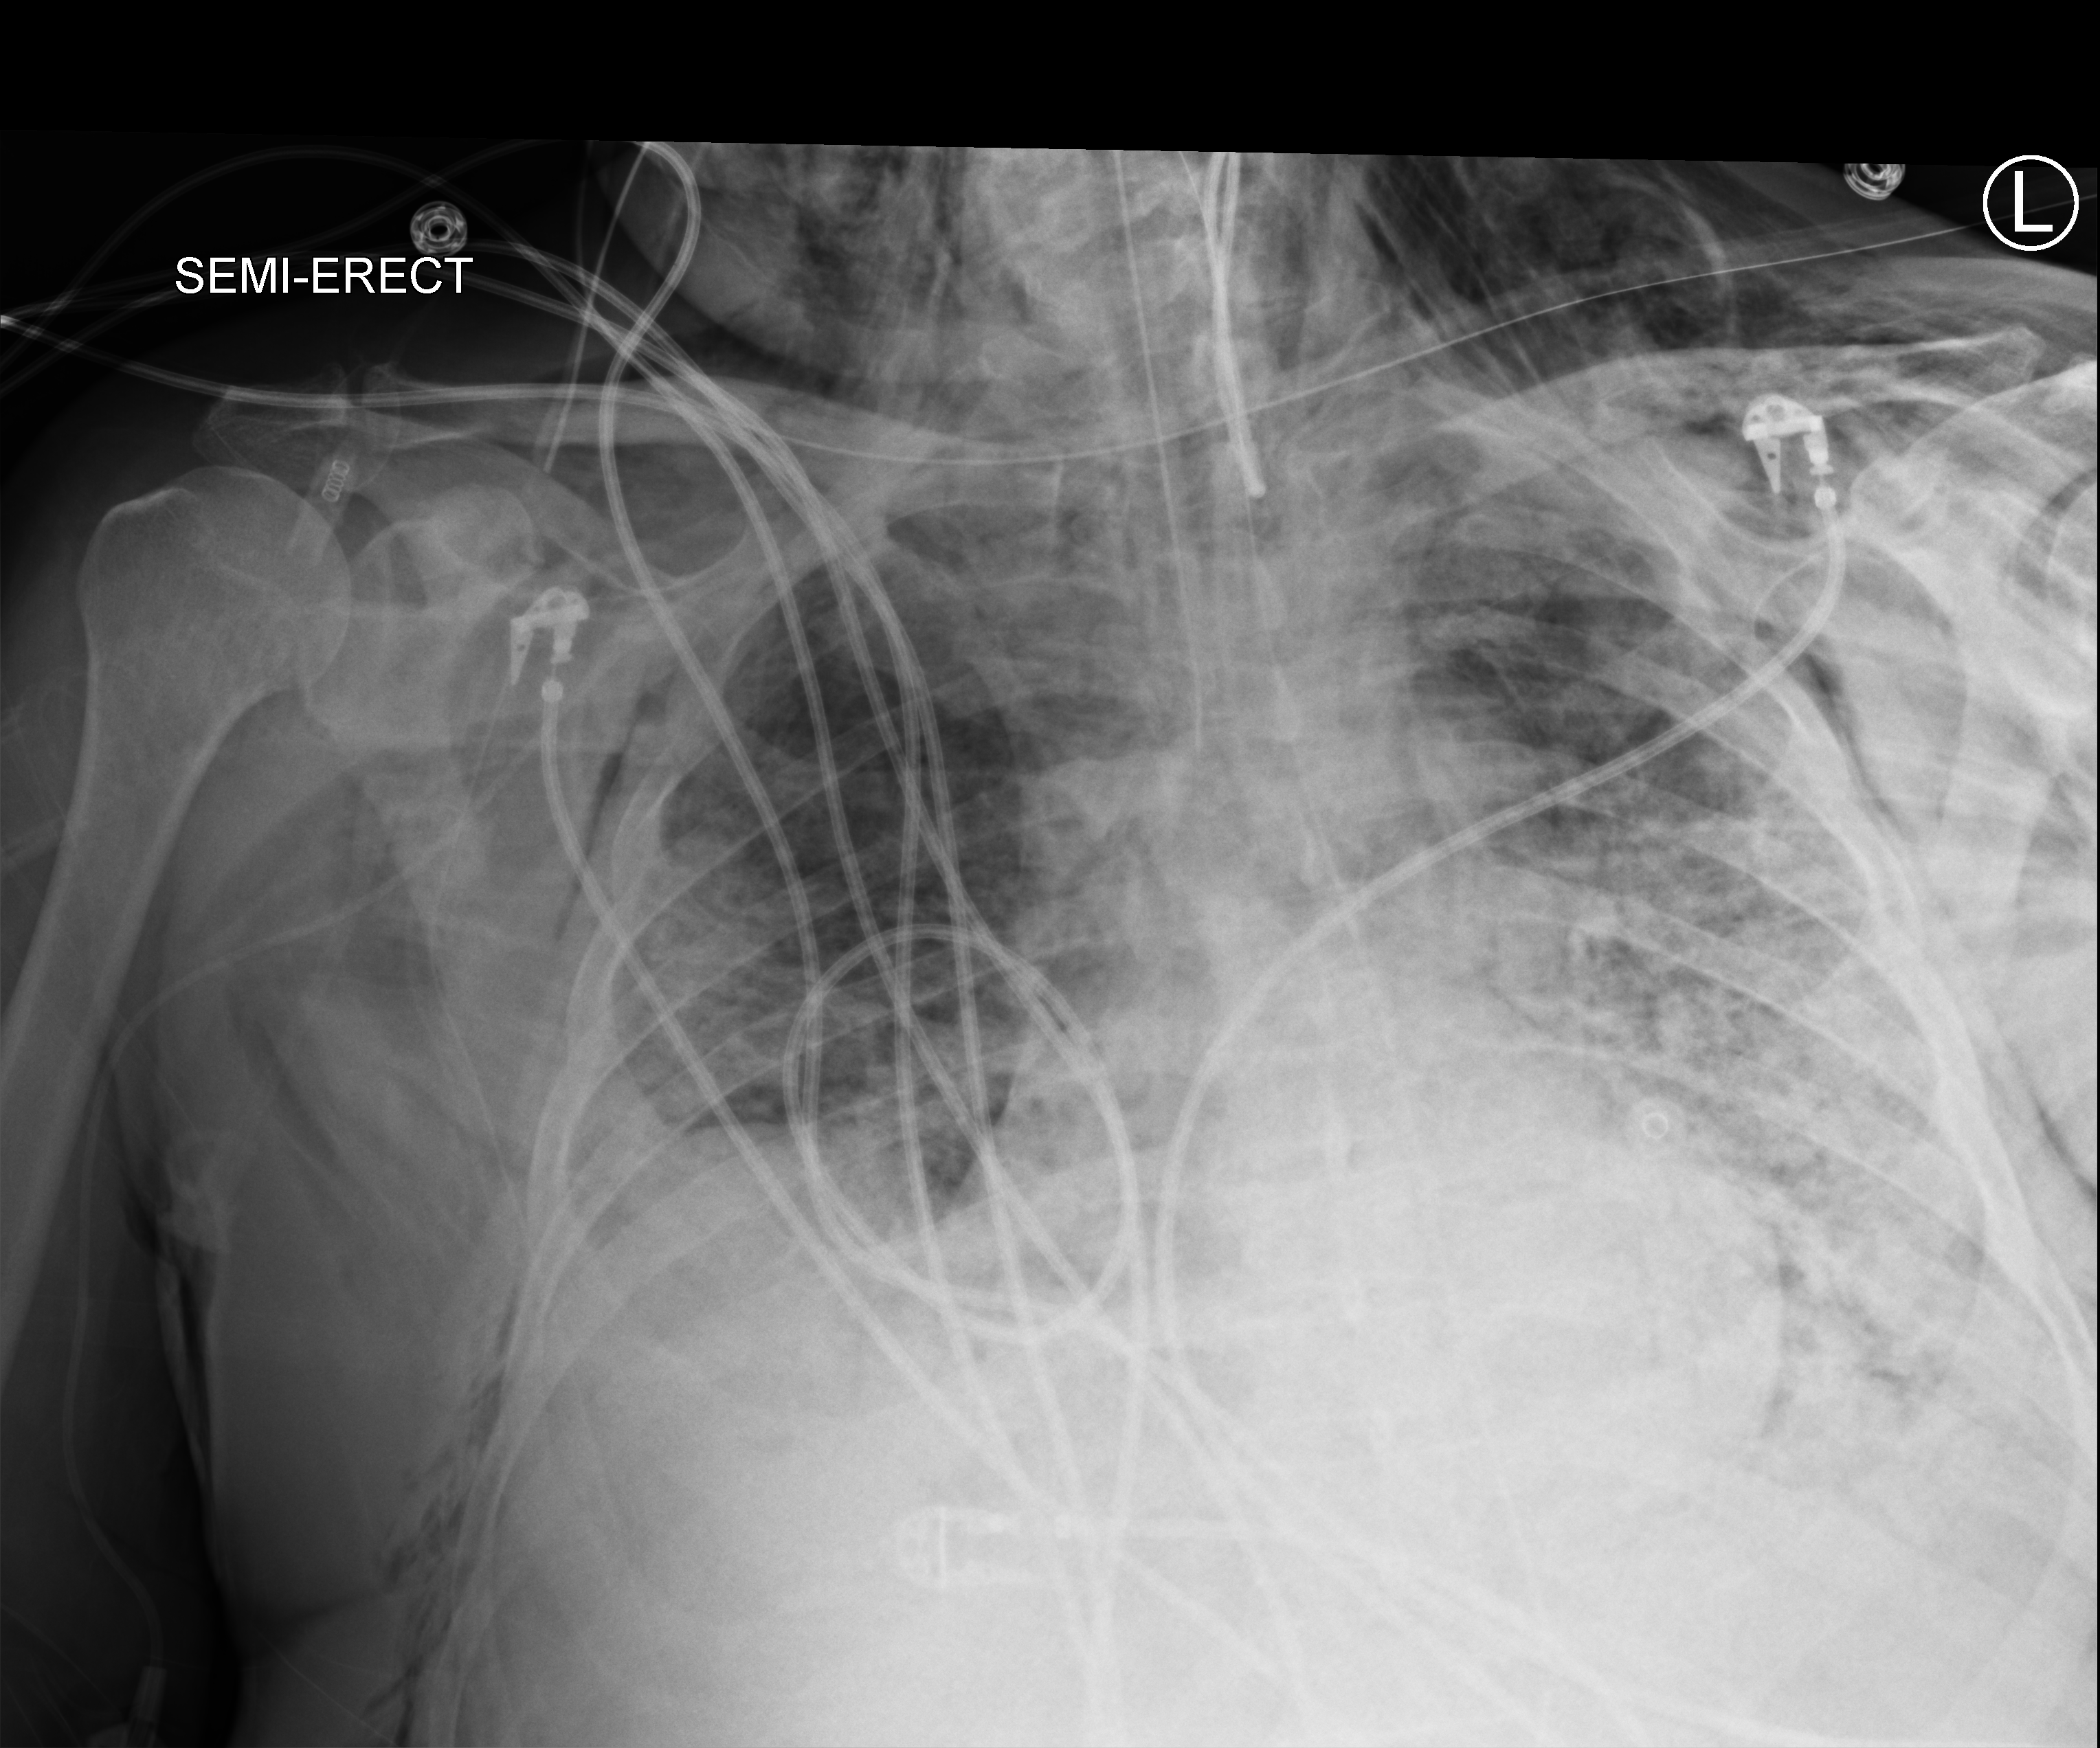
Portable chest radiograph; anteroposterior (AP) projection. Male patient hospitalised with COVID-19, age 60–74 years.
Hospital-stay facts (about this admission, not read from this image; timing relative to this image not recorded):
- mechanically ventilated during this hospital stay: yes